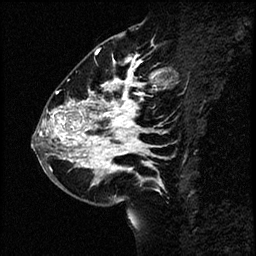
Breast MRI (dynamic contrast-enhanced), one sagittal slice; slice 28 of 60 in the series (ordered by position); dynamic contrast-enhanced study with each time point stored as its own series, time point 2 of 4 at this slice position (early post-contrast, ordered by acquisition time); 1.5 T; TE 4.2 ms, TR 17.6 ms; 256 × 256 image matrix. Female patient, age 43 years. Case-level facts recorded for this patient, not image findings: setting: breast cancer imaged before/during neoadjuvant chemotherapy.
Annotated regions visible in this slice (semi-automatically segmented with operator editing):
- analysis volume of interest (the breast-tissue region the enhancement analysis was run in; not a lesion): bounding box [x1, y1, x2, y2] px = [34, 56, 169, 191]
- tumour enhancement mask (voxels above the 100 % enhancement threshold inside the analysis volume of interest): [40, 56, 158, 180]